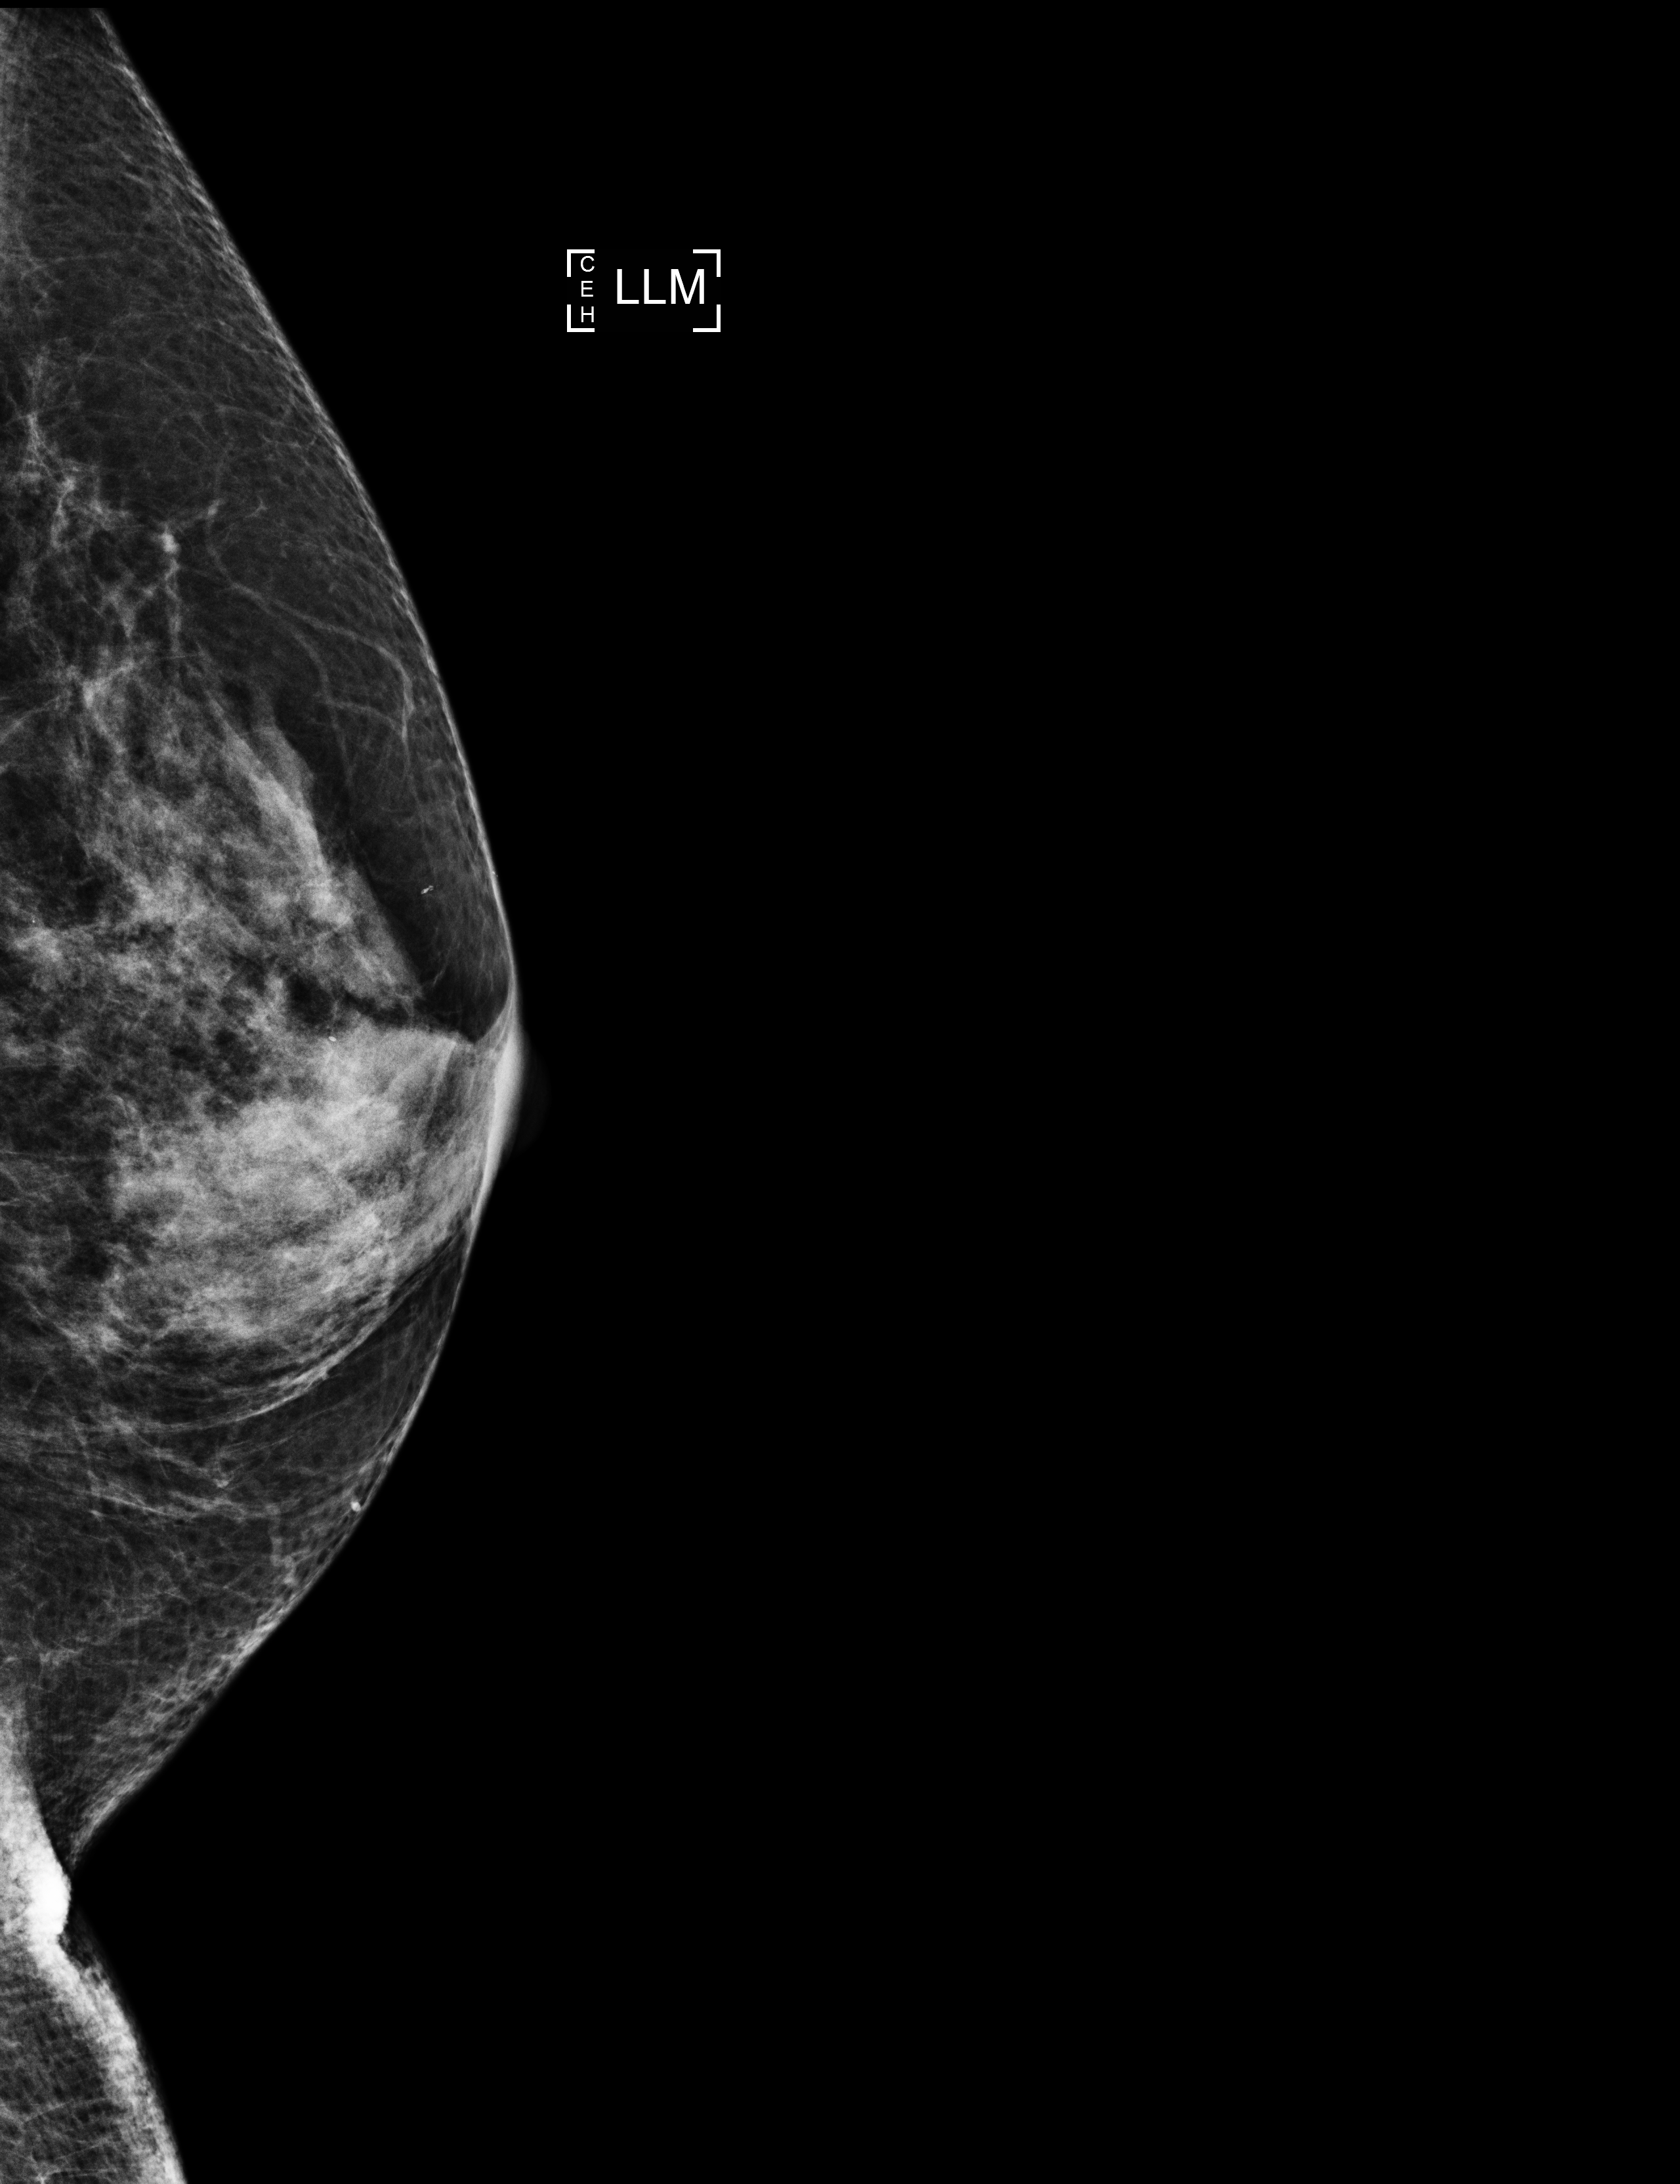
Screening examination, system: Selenia Dimensions. Female patient, age 60 years.
Image type: full-field digital mammogram. Breast: left. Projection: lateromedial (LM) view.